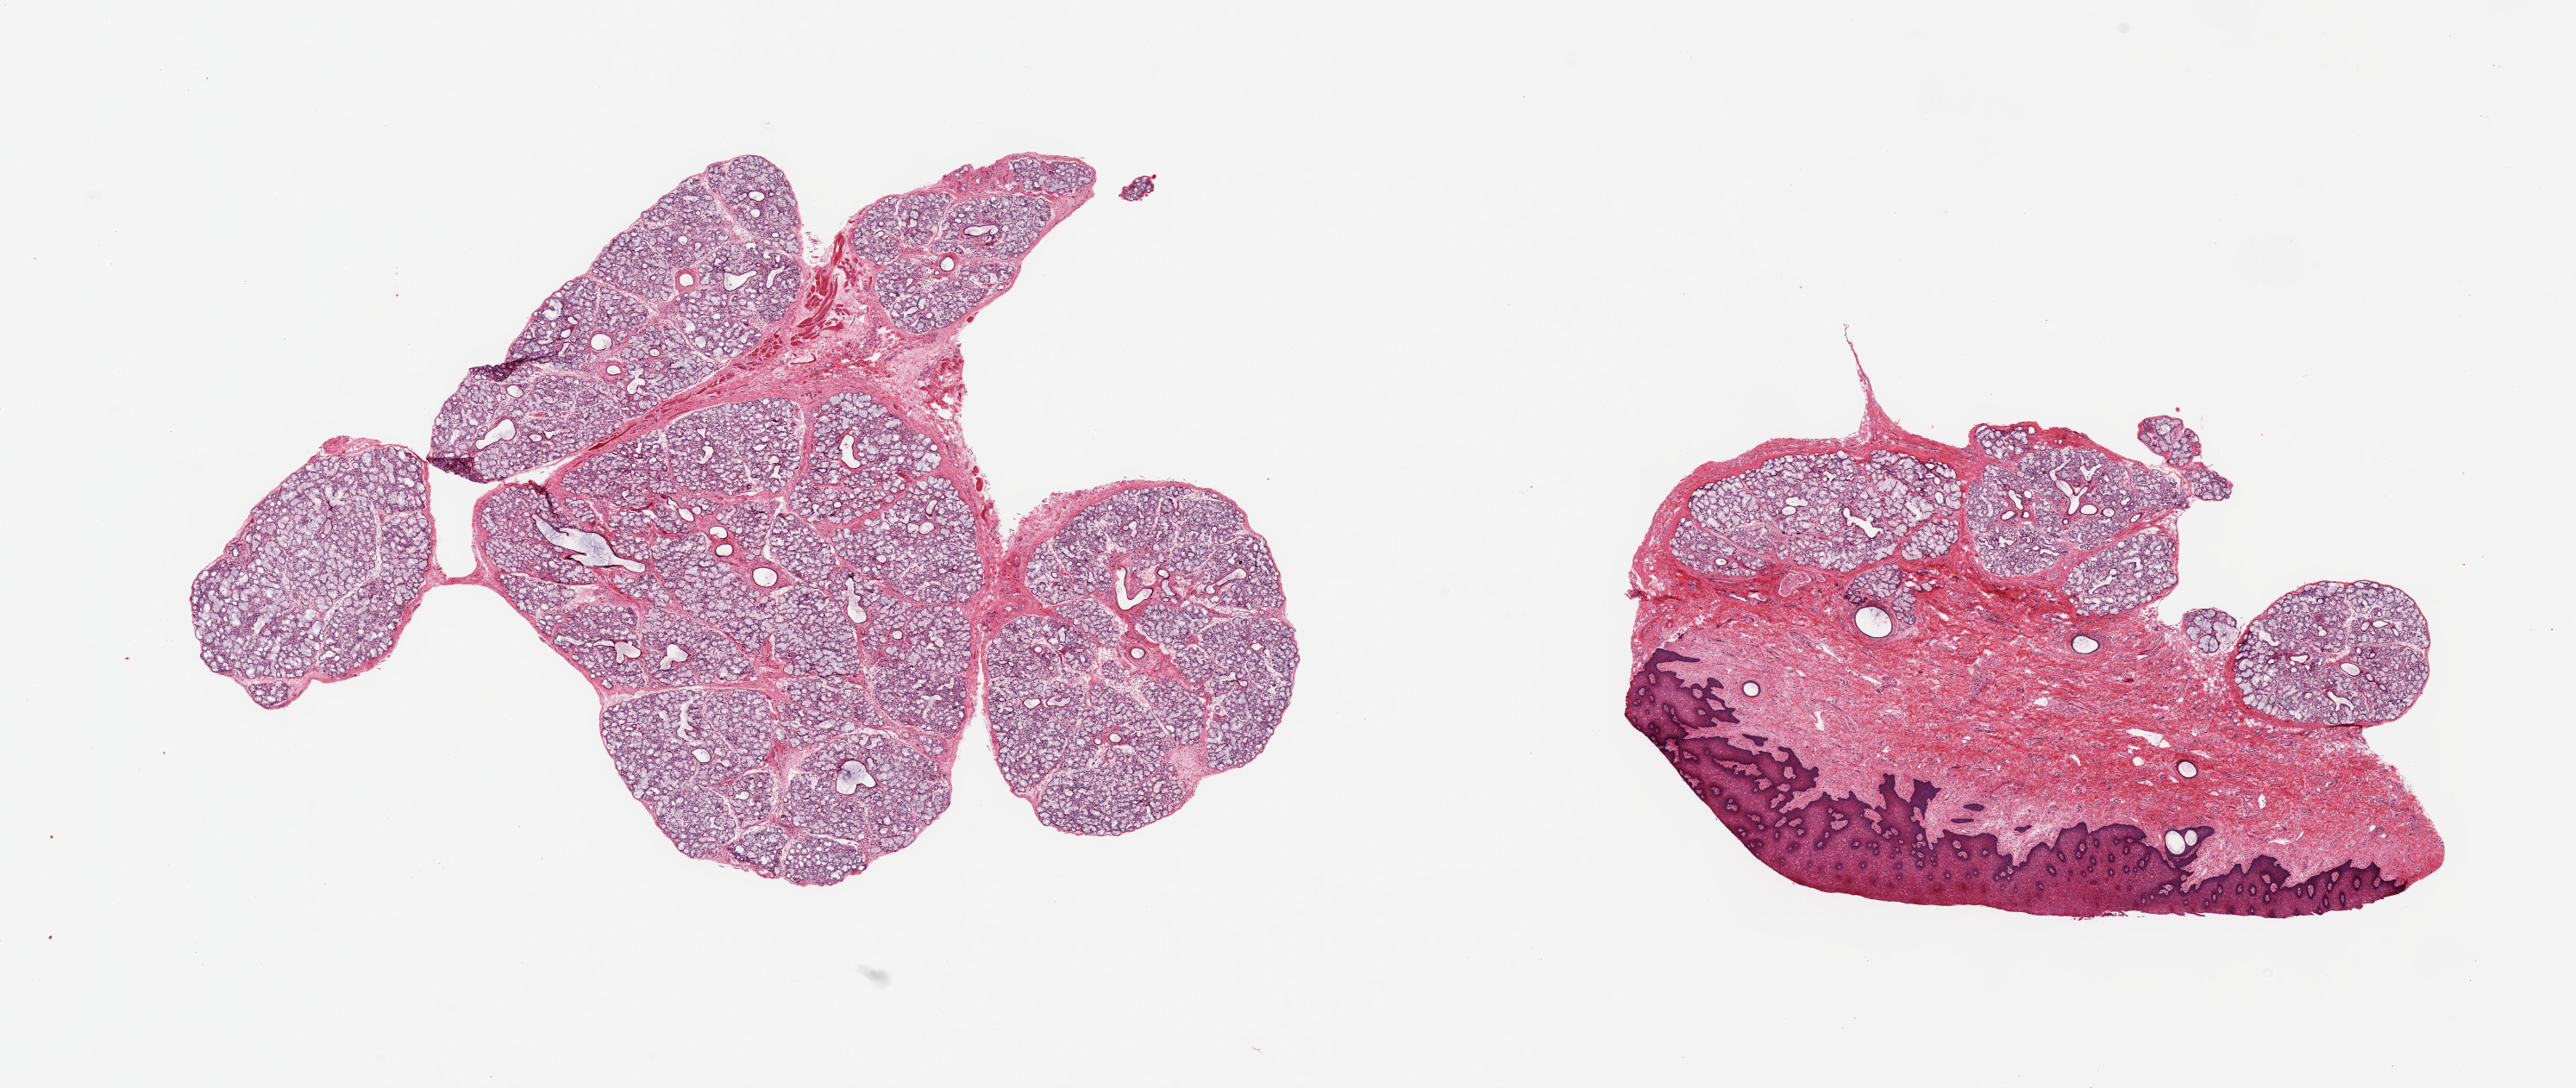
Digitized H&E-stained section — a low-resolution overview of the entire scanned area, about 23.6 x 10.0 mm (from a 20x scan); PAXgene-fixed paraffin-embedded (PFPE) section; target tissue: minor salivary gland; tissue donor sample.
Pathologist's review note for this sample: 2 pieces; mild chronic inflammation, one piece is ~70% stroma and lip.